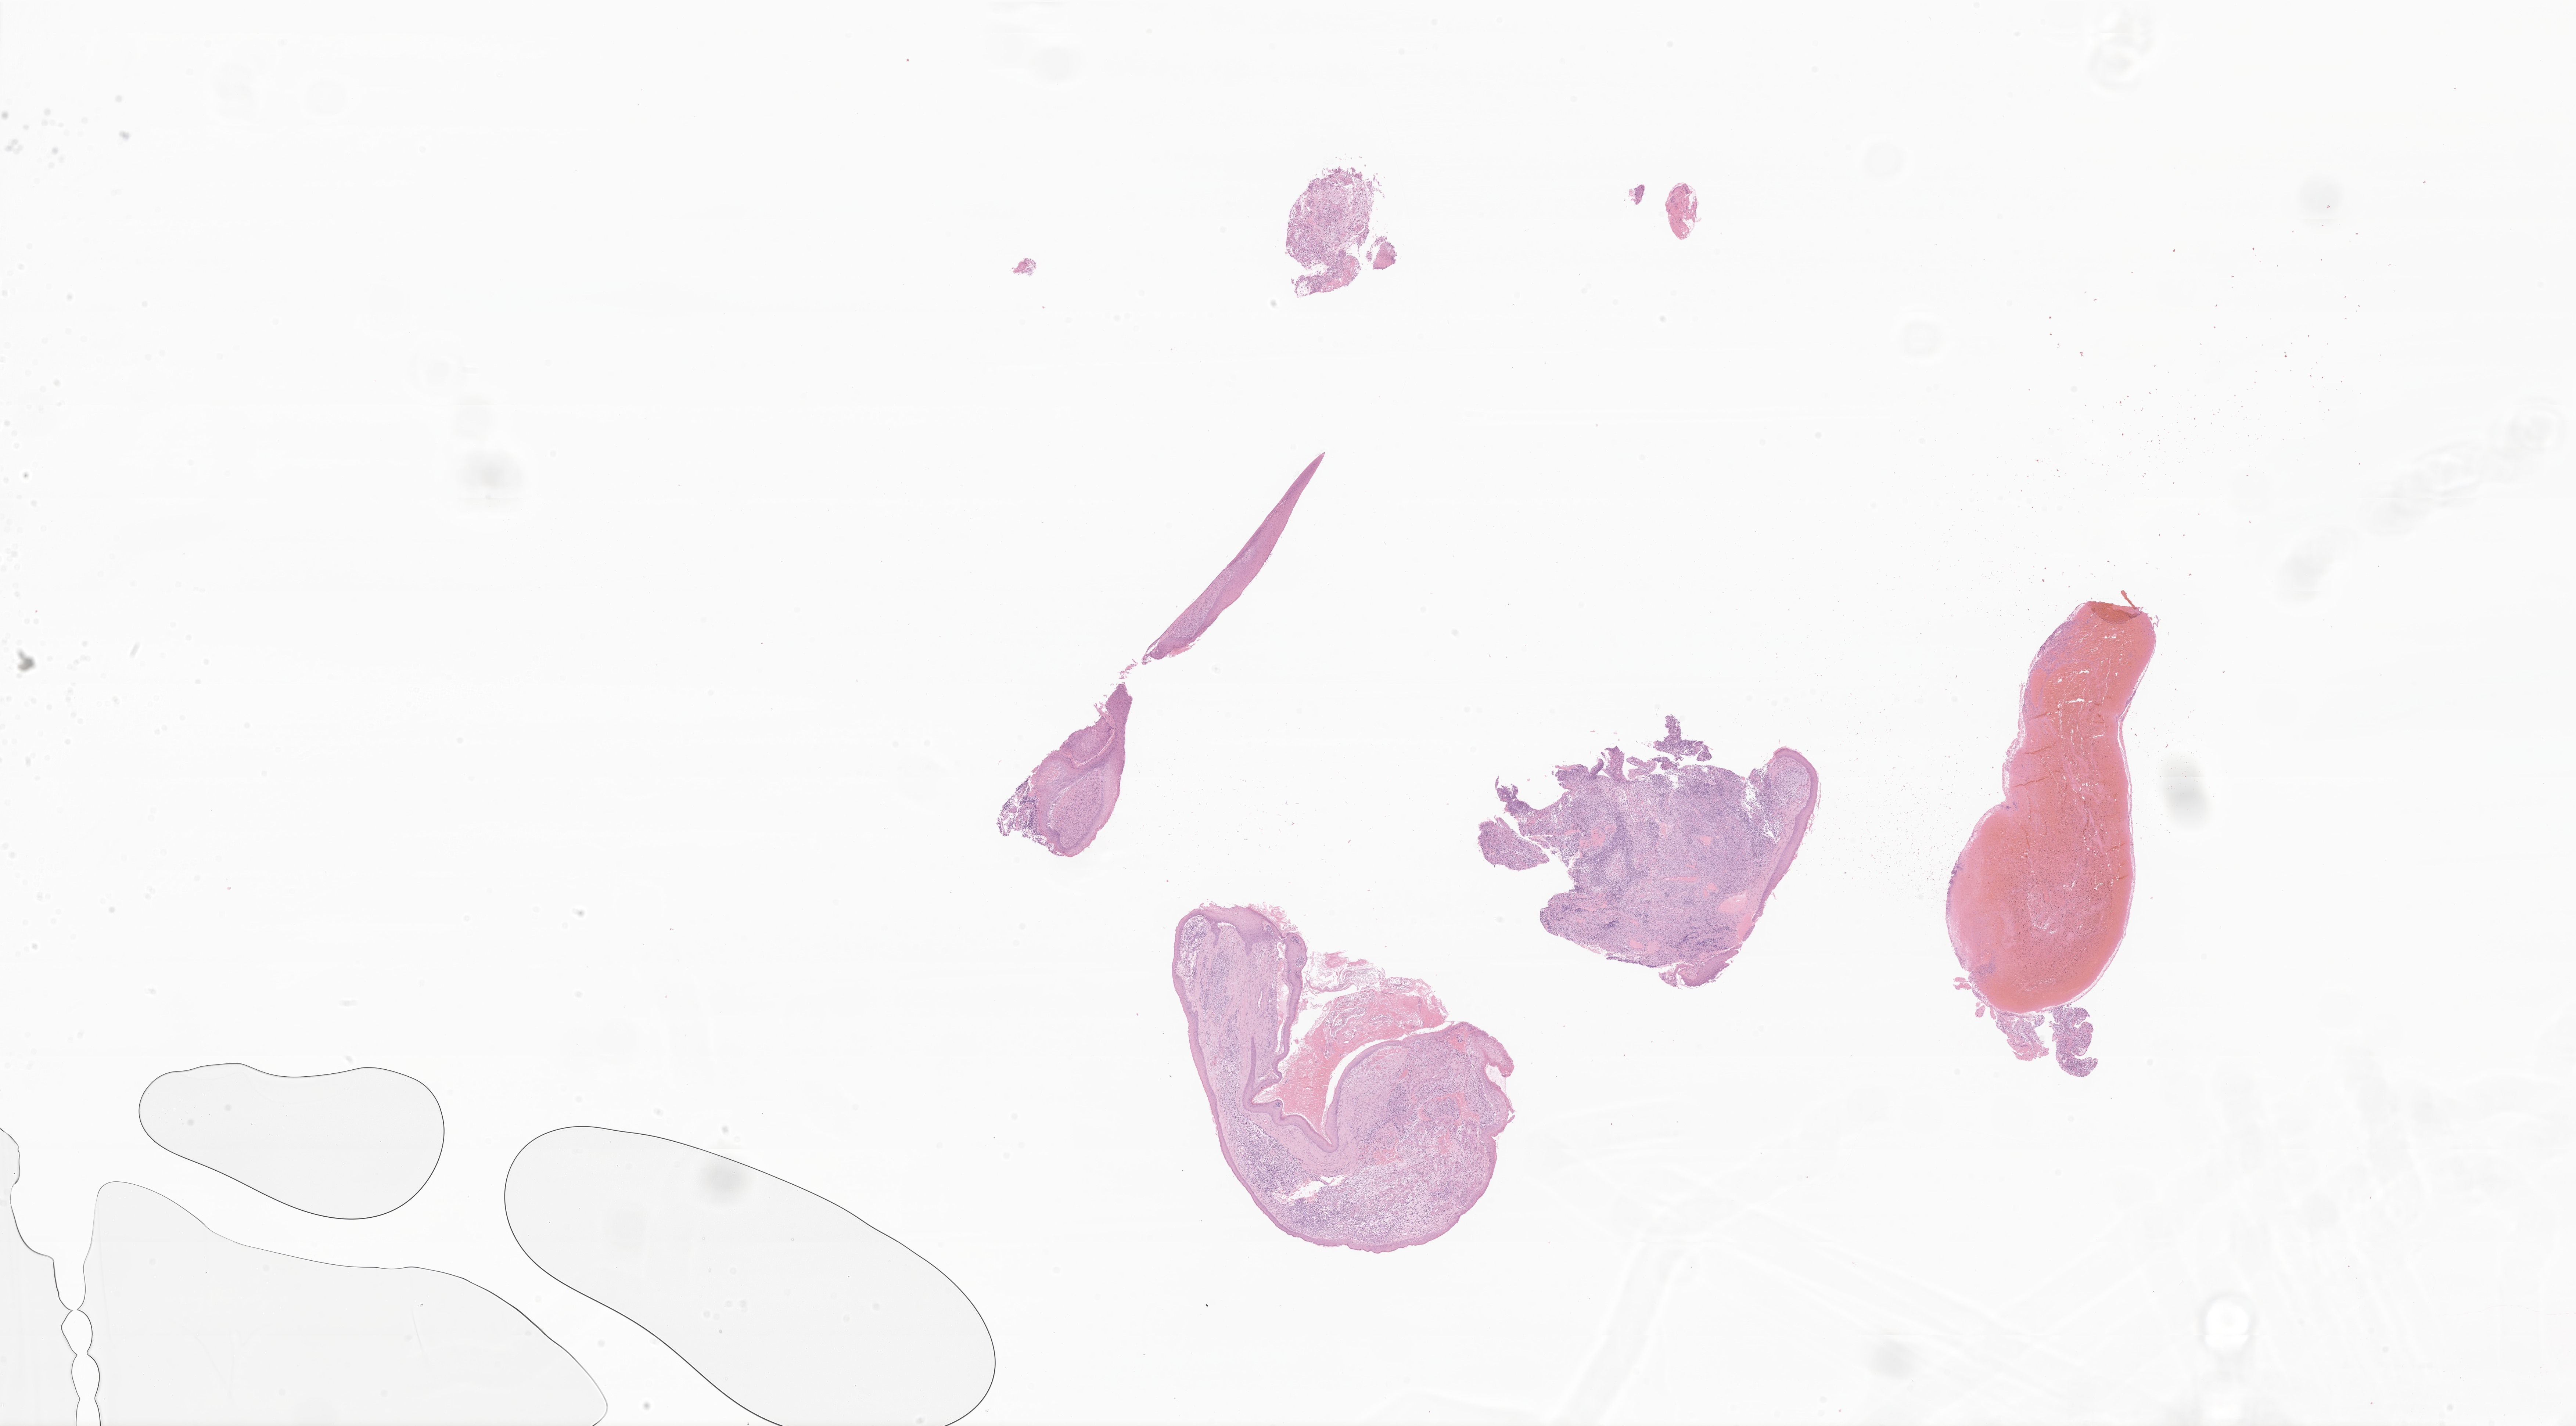
Digitized H&E-stained section of tumor tissue from the cranial and/or facial bone — whole scanned area (about 29.6 x 16.4 mm) shown as a low-resolution overview; formalin-fixed, paraffin-embedded (FFPE) tissue. Male patient, age 60 months (5 years).
* diagnosis (ICD-O-3 morphology term): Embryonal rhabdomyosarcoma, NOS